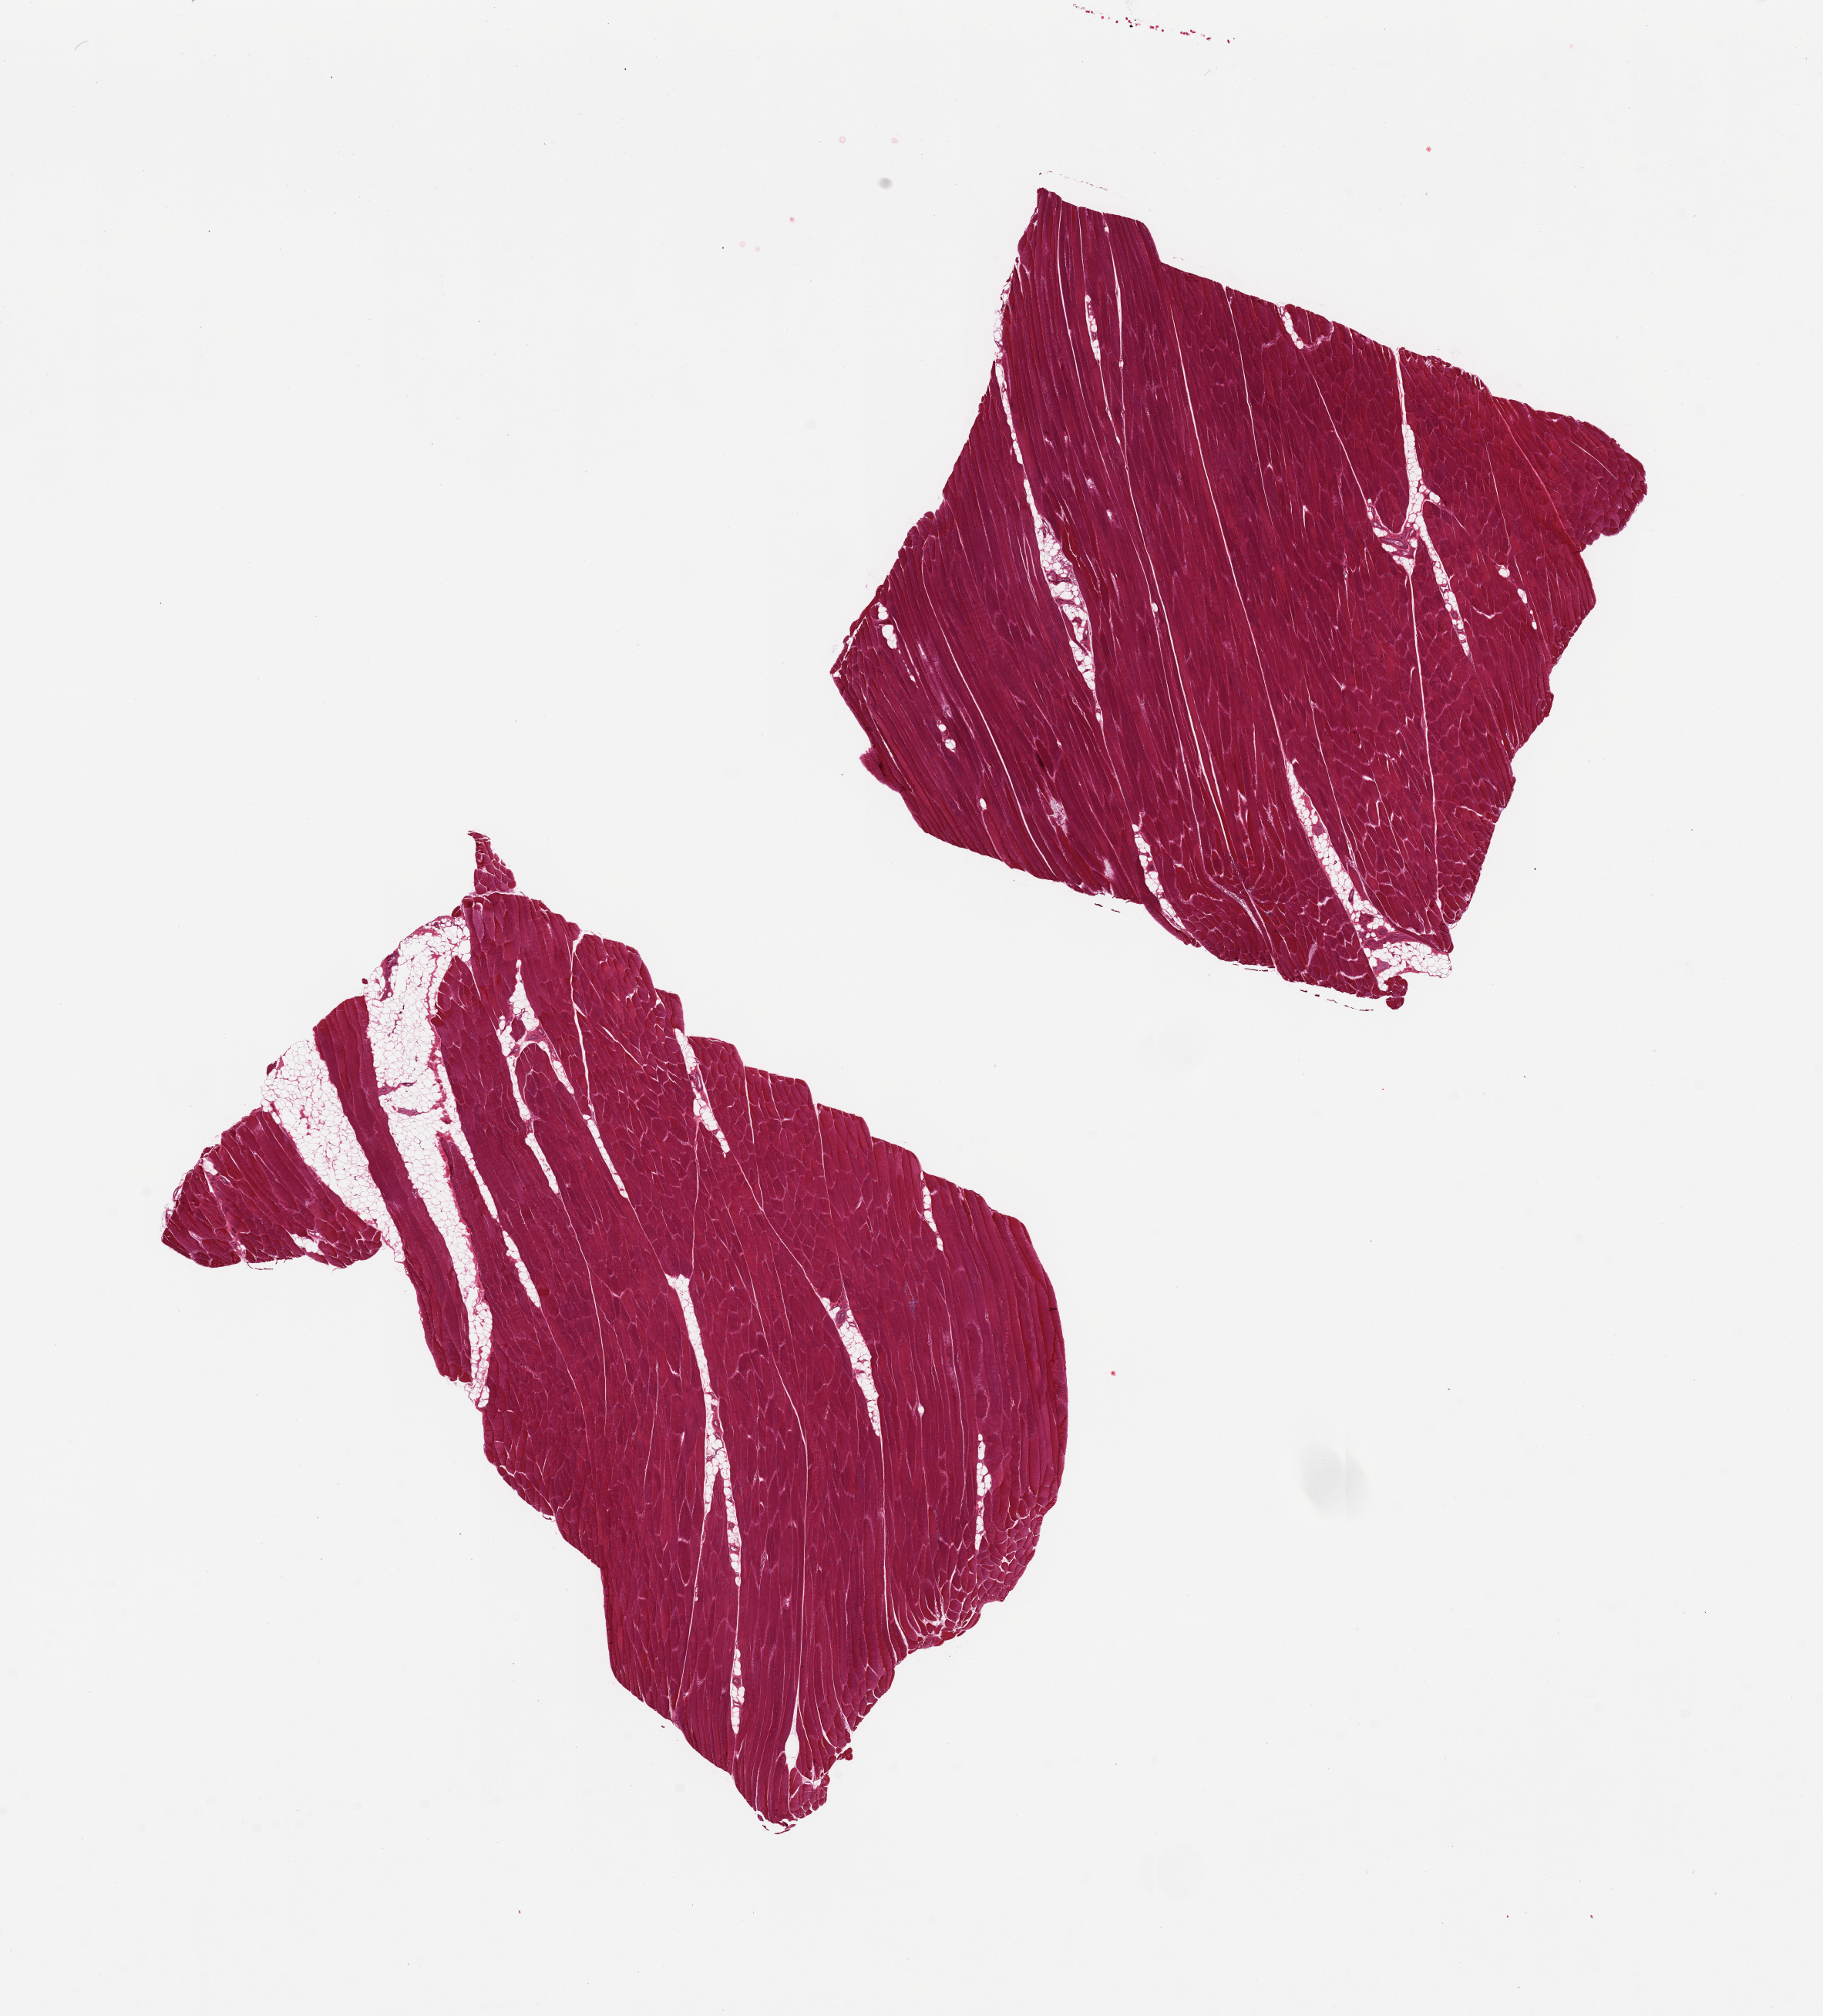
Digitized H&E-stained section, whole scanned area (about 18.7 x 20.7 mm) shown as a low-resolution overview; PAXgene-fixed paraffin-embedded (PFPE) section; target tissue: skeletal muscle; donor tissue sample. Donor: male.
Review note (as recorded): 2 pieces. 10% fat in 1 piece.